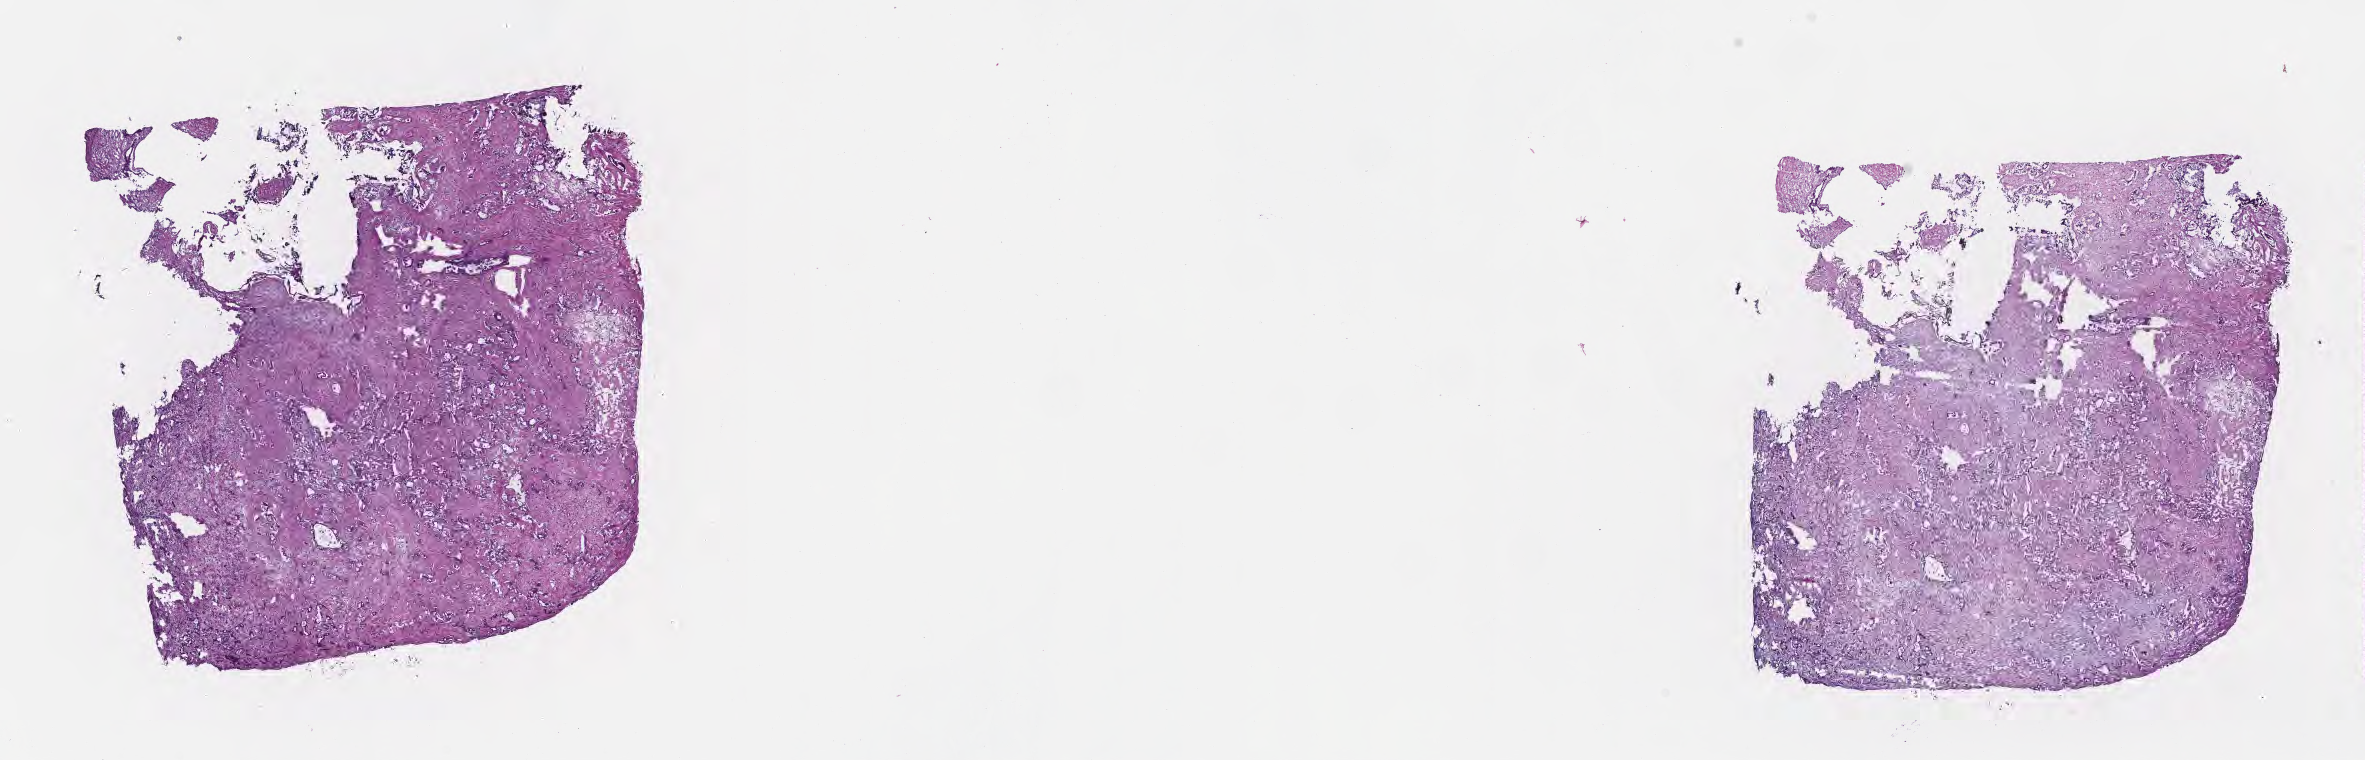
Whole-slide image, H&E stain, low-resolution overview of the scanned area, about 19.1 x 6.1 mm, cryosection, specimen: primary tumor, site: extrahepatic bile duct. Patient: male, age at initial diagnosis 62 years. Tumor grade: G2 (moderately differentiated). Slide review estimates, as recorded: tumor cells 80%, tumor nuclei 80%, stromal cells 20%, necrosis 0%, normal cells 0%. Infiltration values recorded for this section: lymphocyte infiltration 4%, monocyte infiltration 2%, neutrophil infiltration 6%.
AJCC pathologic stage: Stage IV. Histologic diagnosis: Cholangiocarcinoma.